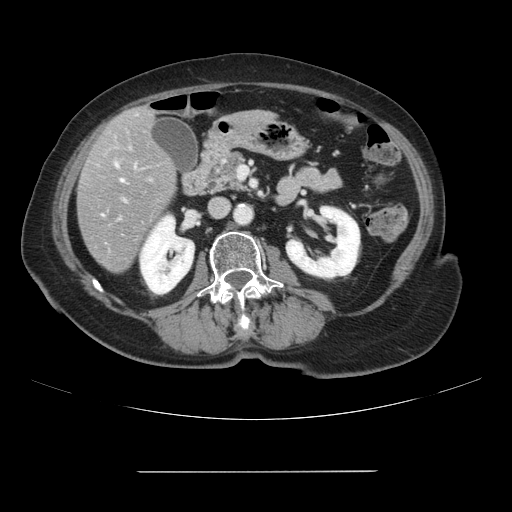
Contrast-enhanced abdominal CT, one axial slice. Slice 30 of 111 in the series (ordered by position). 120 kVp. Intravenous contrast given. Soft-tissue window (W 400 / L 40 HU). 2.5 mm slice thickness. 512 × 512 image matrix. Female patient, age 74 years. From the clinical record (not read from this slice): diagnosis: colorectal cancer liver metastases, imaged before liver resection; multiple liver metastases: yes; largest metastasis: 1.1 cm; chemotherapy before resection: yes.
Structures marked on this image (outlined manually by an expert reader):
- hepatic veins: bounding box <116,164,123,182> (left, top, right, bottom; pixels)
- liver: <78,107,176,273>
- planned liver remnant (the part of the liver to remain after resection): <142,108,155,121>